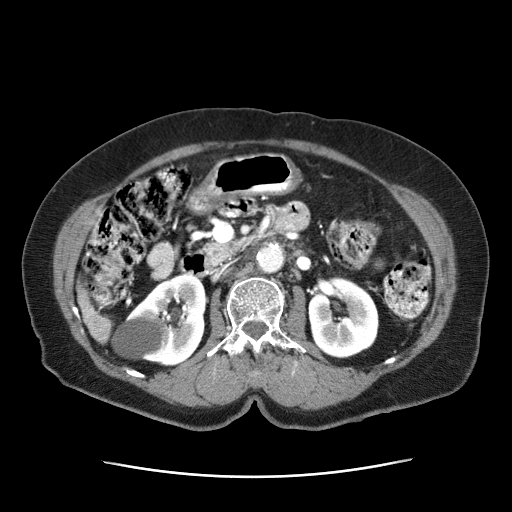
Contrast-enhanced abdominal CT (liver protocol), one axial slice; slice 9 of 63 in the series (ordered by position); reconstruction kernel STANDARD; 120 kVp; intravenous contrast given; soft-tissue window (W 400 / L 40 HU); 2.5 mm slice thickness; 512 × 512 image matrix, field of view 360 × 360 mm. Female patient, age 79 years. From the clinical record (not read from this slice): diagnosis: hepatocellular carcinoma (patient treated with transarterial chemoembolisation; whether this scan precedes or follows treatment is not stated here); TNM stage (as recorded): Stage-II; Child-Pugh class: B; tumour differentiation: well differentiated; tumour size: 5 cm.
Structures marked on this image (semi-automatically segmented with operator editing):
- abdominal aorta: bounding box [x1, y1, x2, y2] px = [256, 243, 285, 273]
- liver parenchyma outside the tumour (the mass and vessels are separate outlines, so this box may not span the whole liver): [79, 294, 112, 343]